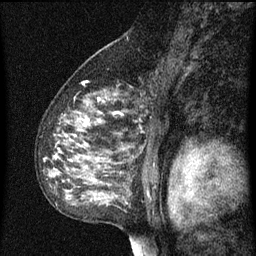
Breast MRI (dynamic contrast-enhanced), one sagittal slice. Position 46 of 60 along the scan axis. Dynamic contrast-enhanced series, image 2 of 3 at this slice position (ordered by acquisition). 1.5 T. TE 4.2 ms, TR 8 ms. 256 × 256 image matrix, field of view 180 × 180 mm. Patient: female, 55 years.
Structures marked on this image (semi-automatically segmented with operator editing):
- analysis volume of interest (the breast-tissue region the enhancement analysis was run in; not a lesion): bounding box [x1, y1, x2, y2] px = [40, 78, 159, 151]
- tumour enhancement mask (voxels above the 70 % enhancement threshold inside the analysis volume of interest): [56, 100, 123, 151]